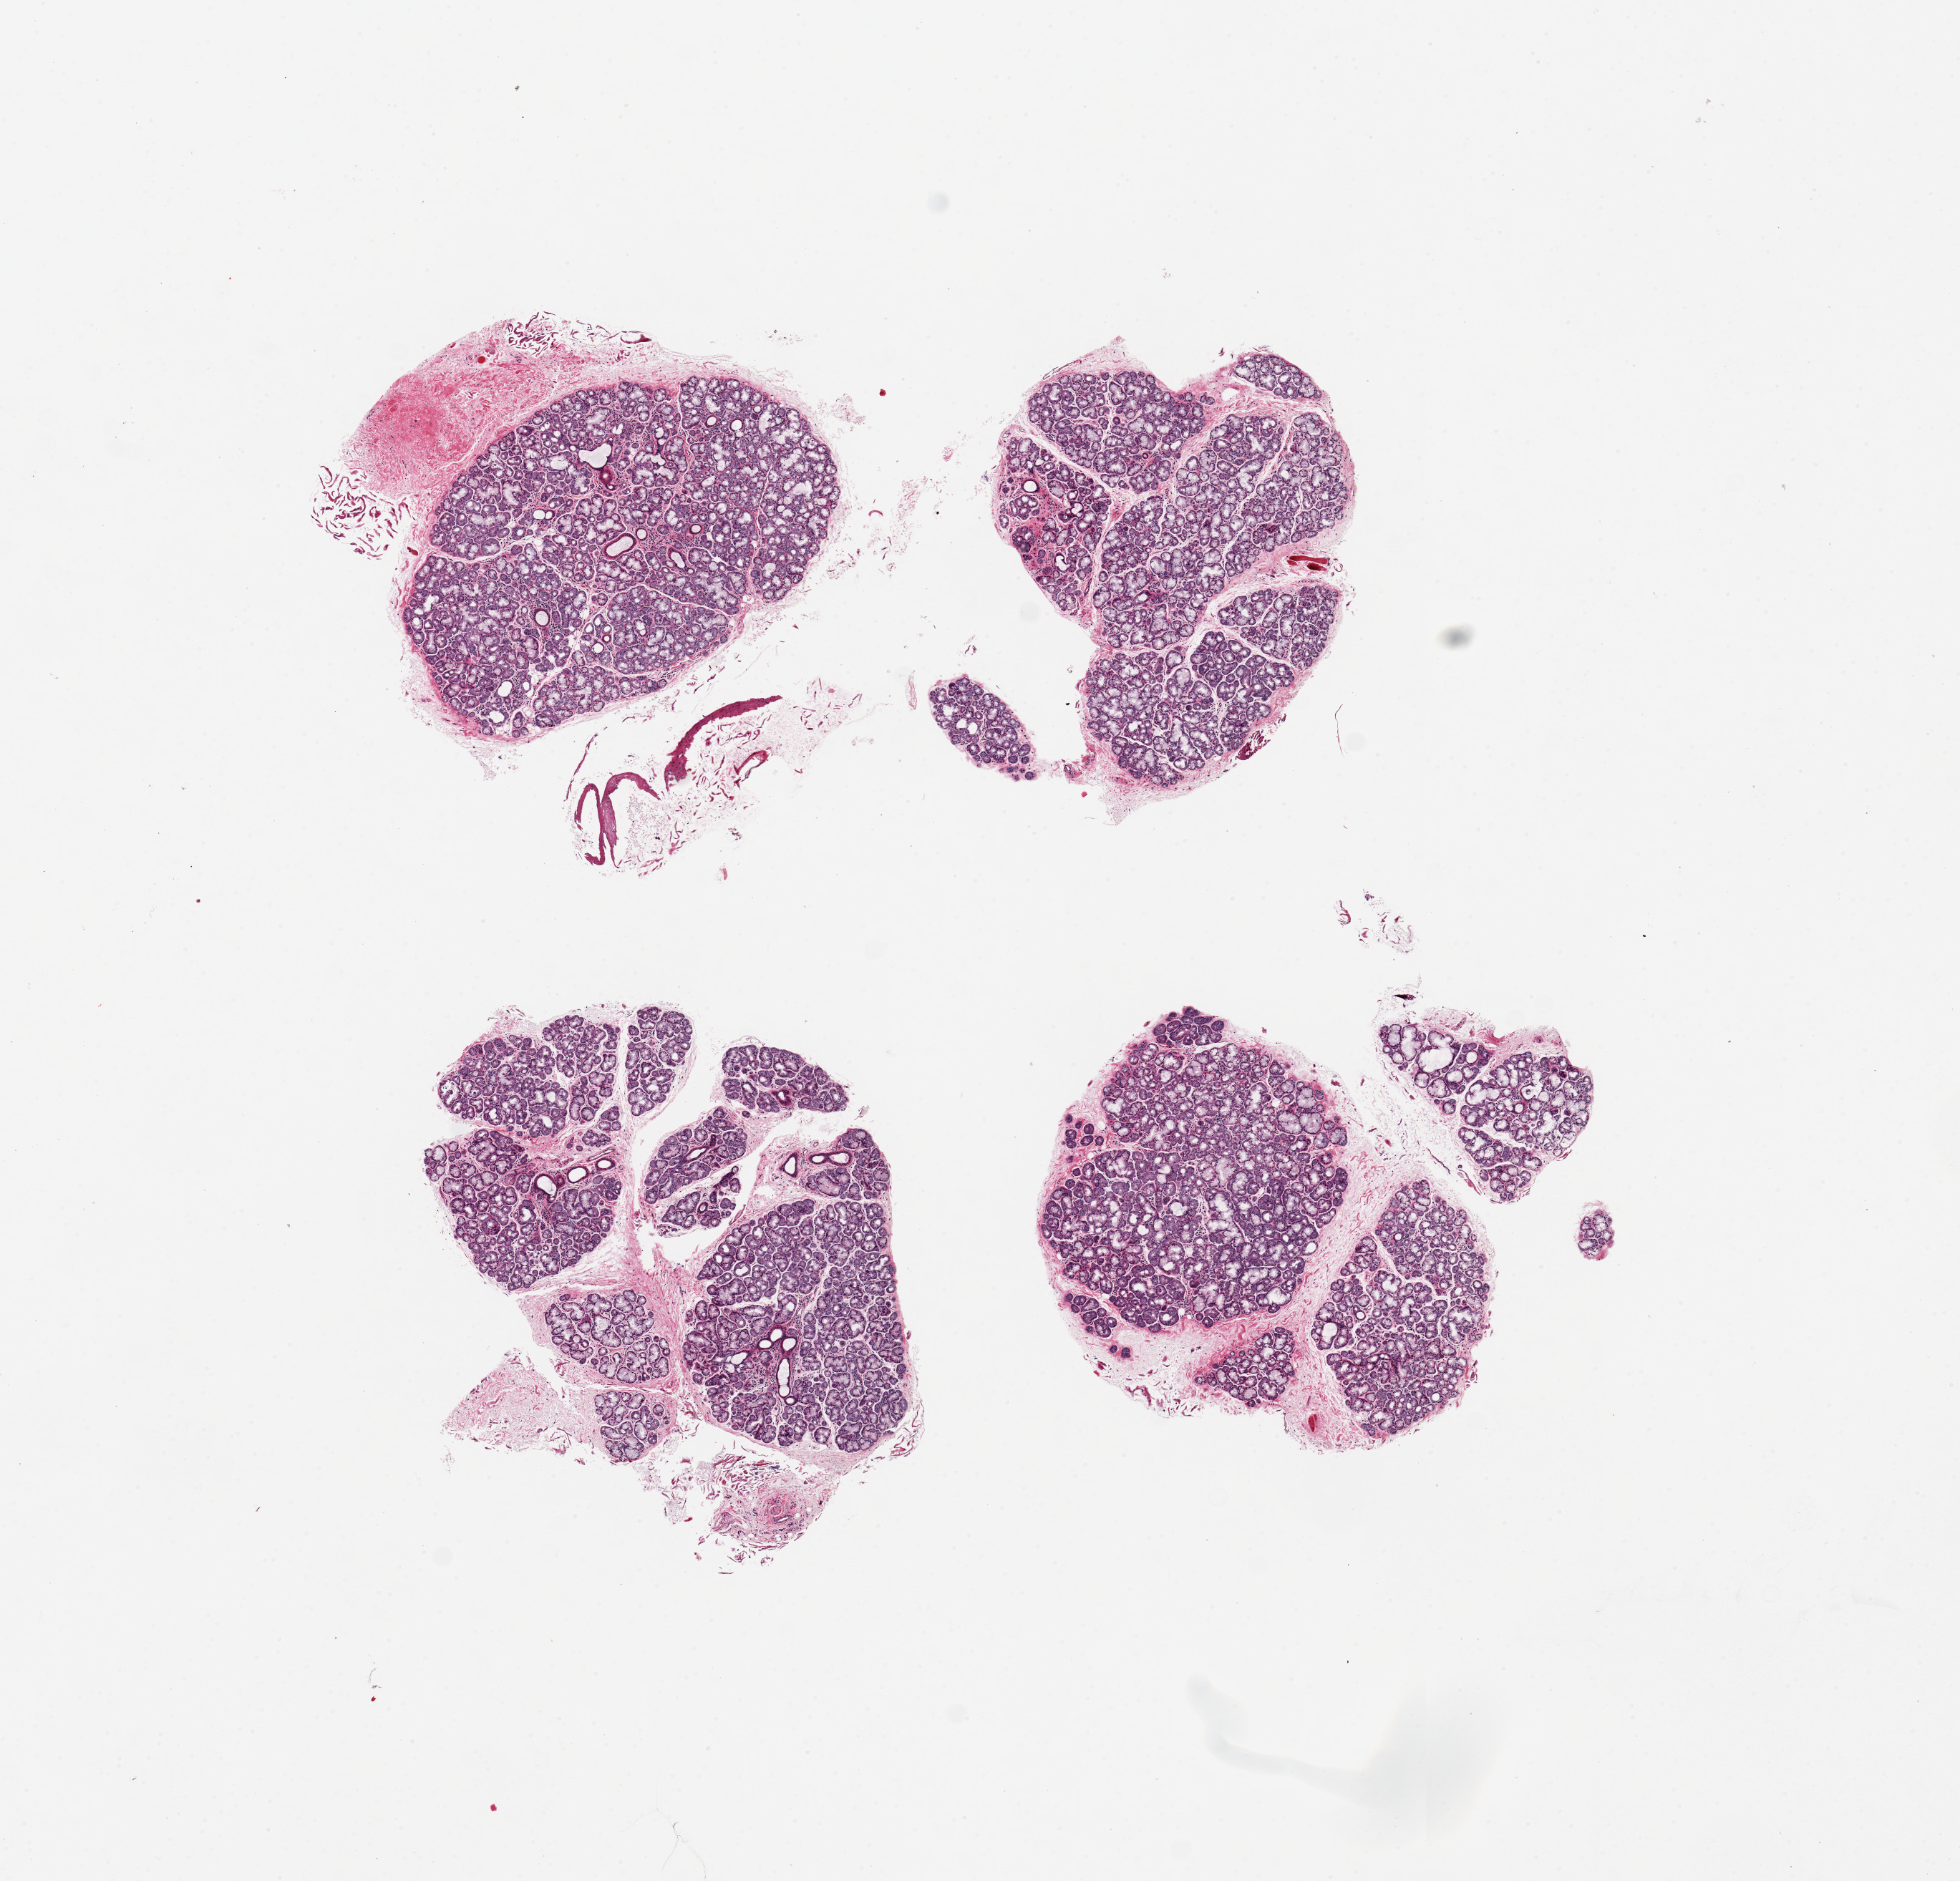
Whole-slide image, haematoxylin and eosin stain, whole scanned area (about 10.8 x 10.4 mm, acquisition: 20x scan) shown as a low-resolution overview; PAXgene-fixed paraffin-embedded (PFPE) section; sampled site (target tissue): minor salivary gland; tissue donor sample. Male donor.
- pathologist's review note for this sample: 4 pieces; well dissected